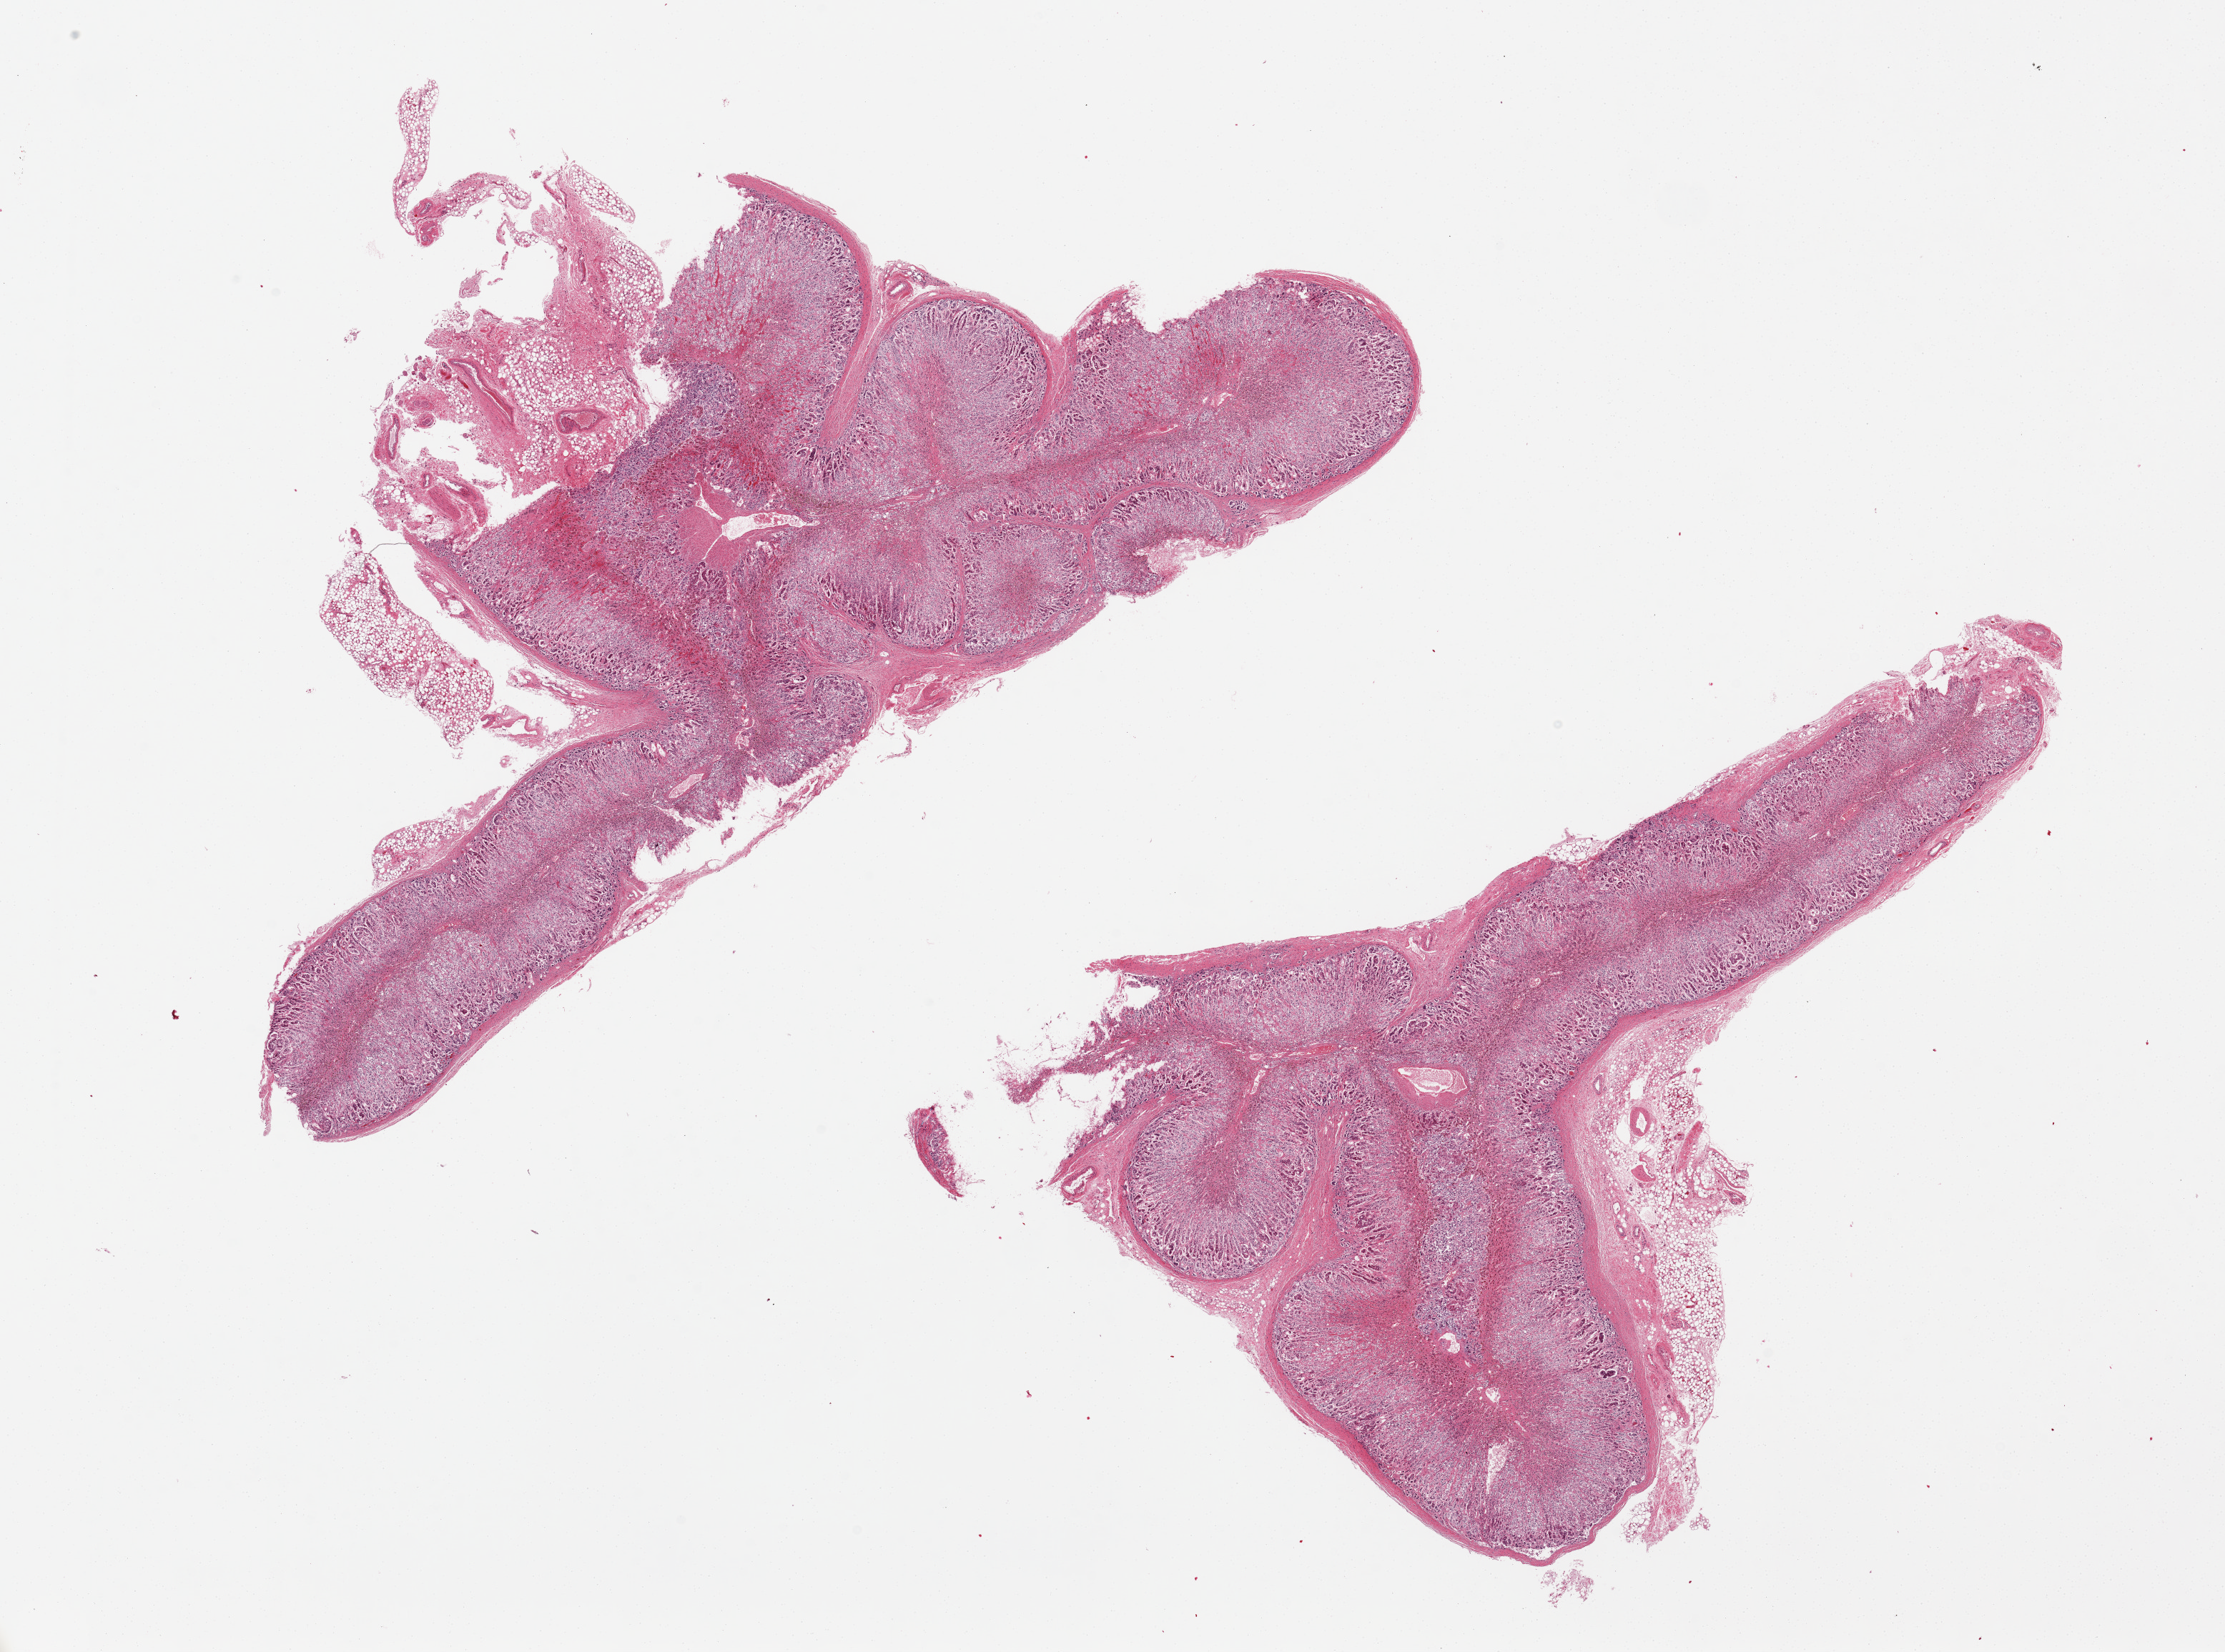
Whole-slide image, haematoxylin and eosin stain — low-resolution overview of the scanned area, about 24.6 x 18.3 mm (acquisition: 20x scan). PAXgene-fixed, paraffin-embedded tissue. Target tissue: adrenal gland. Tissue donor sample. Donor sex: male.
Pathologist's review note for this sample: 2 pieces.